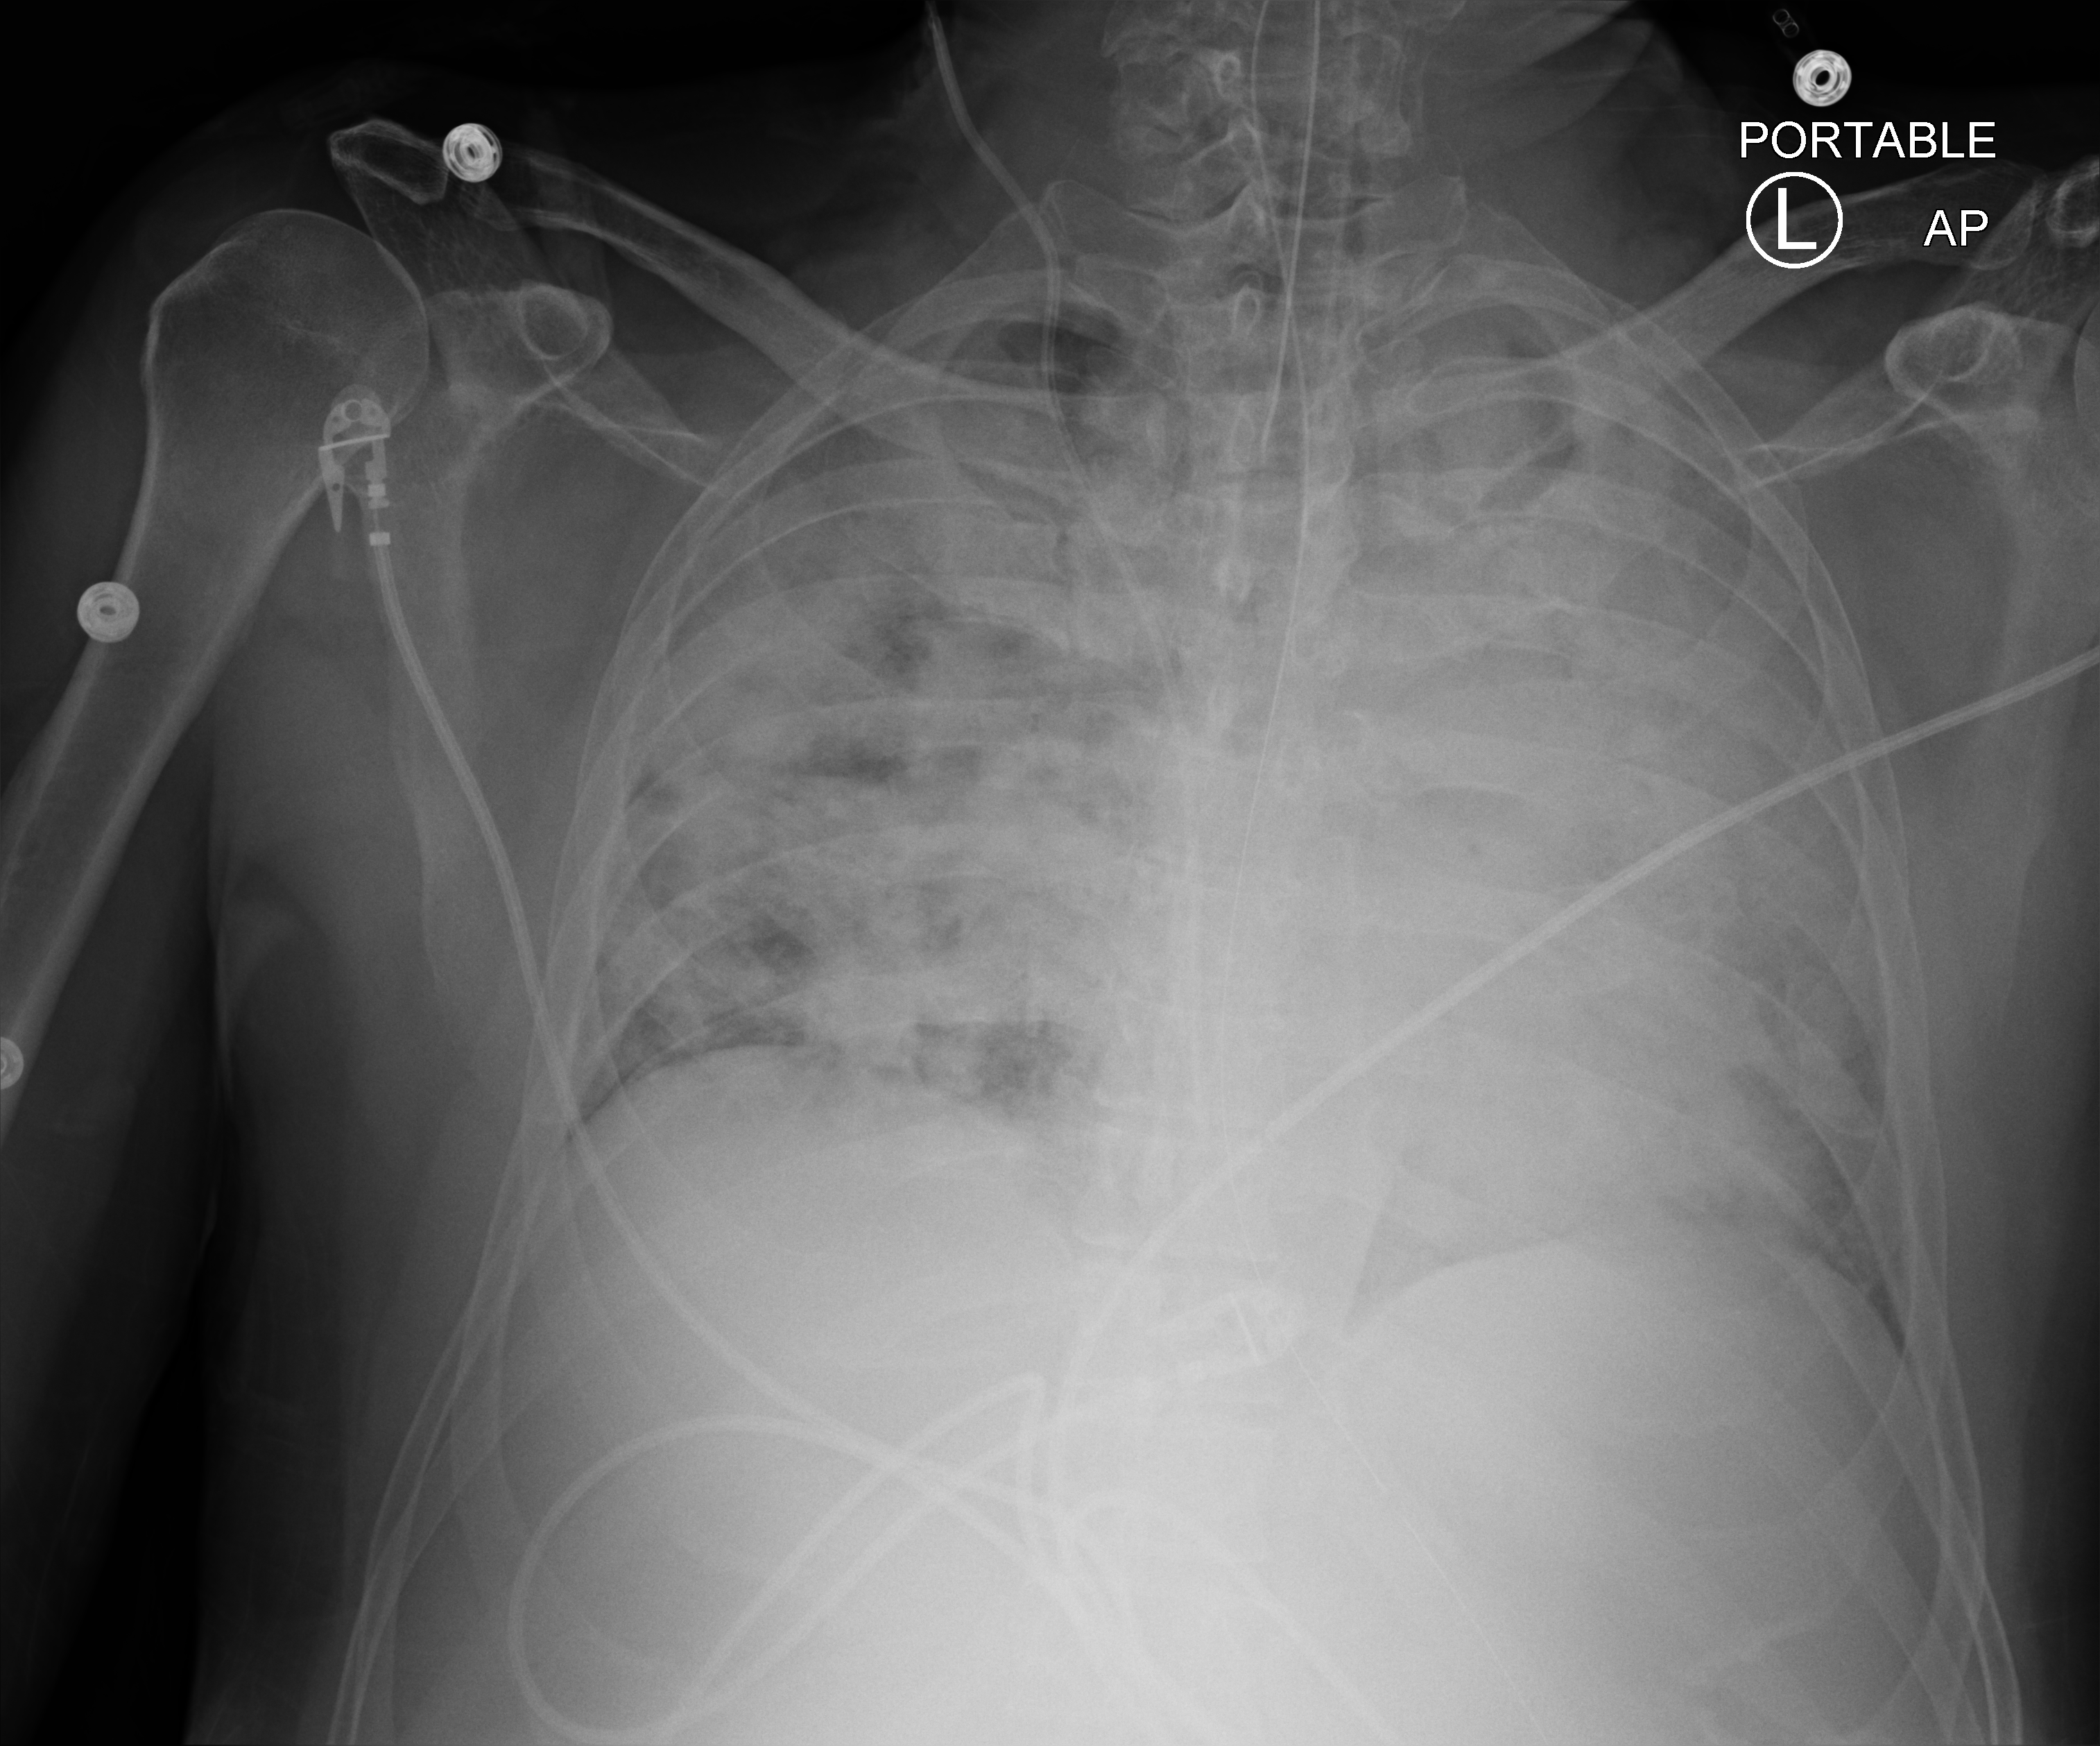
Bedside chest radiograph (computed radiography). Patient hospitalised with COVID-19; male, aged 18–59 years.
Hospital-stay facts (about this admission, not read from this image; timing relative to this image not recorded):
- mechanically ventilated during this hospital stay: yes
- length of hospital stay: 25 days